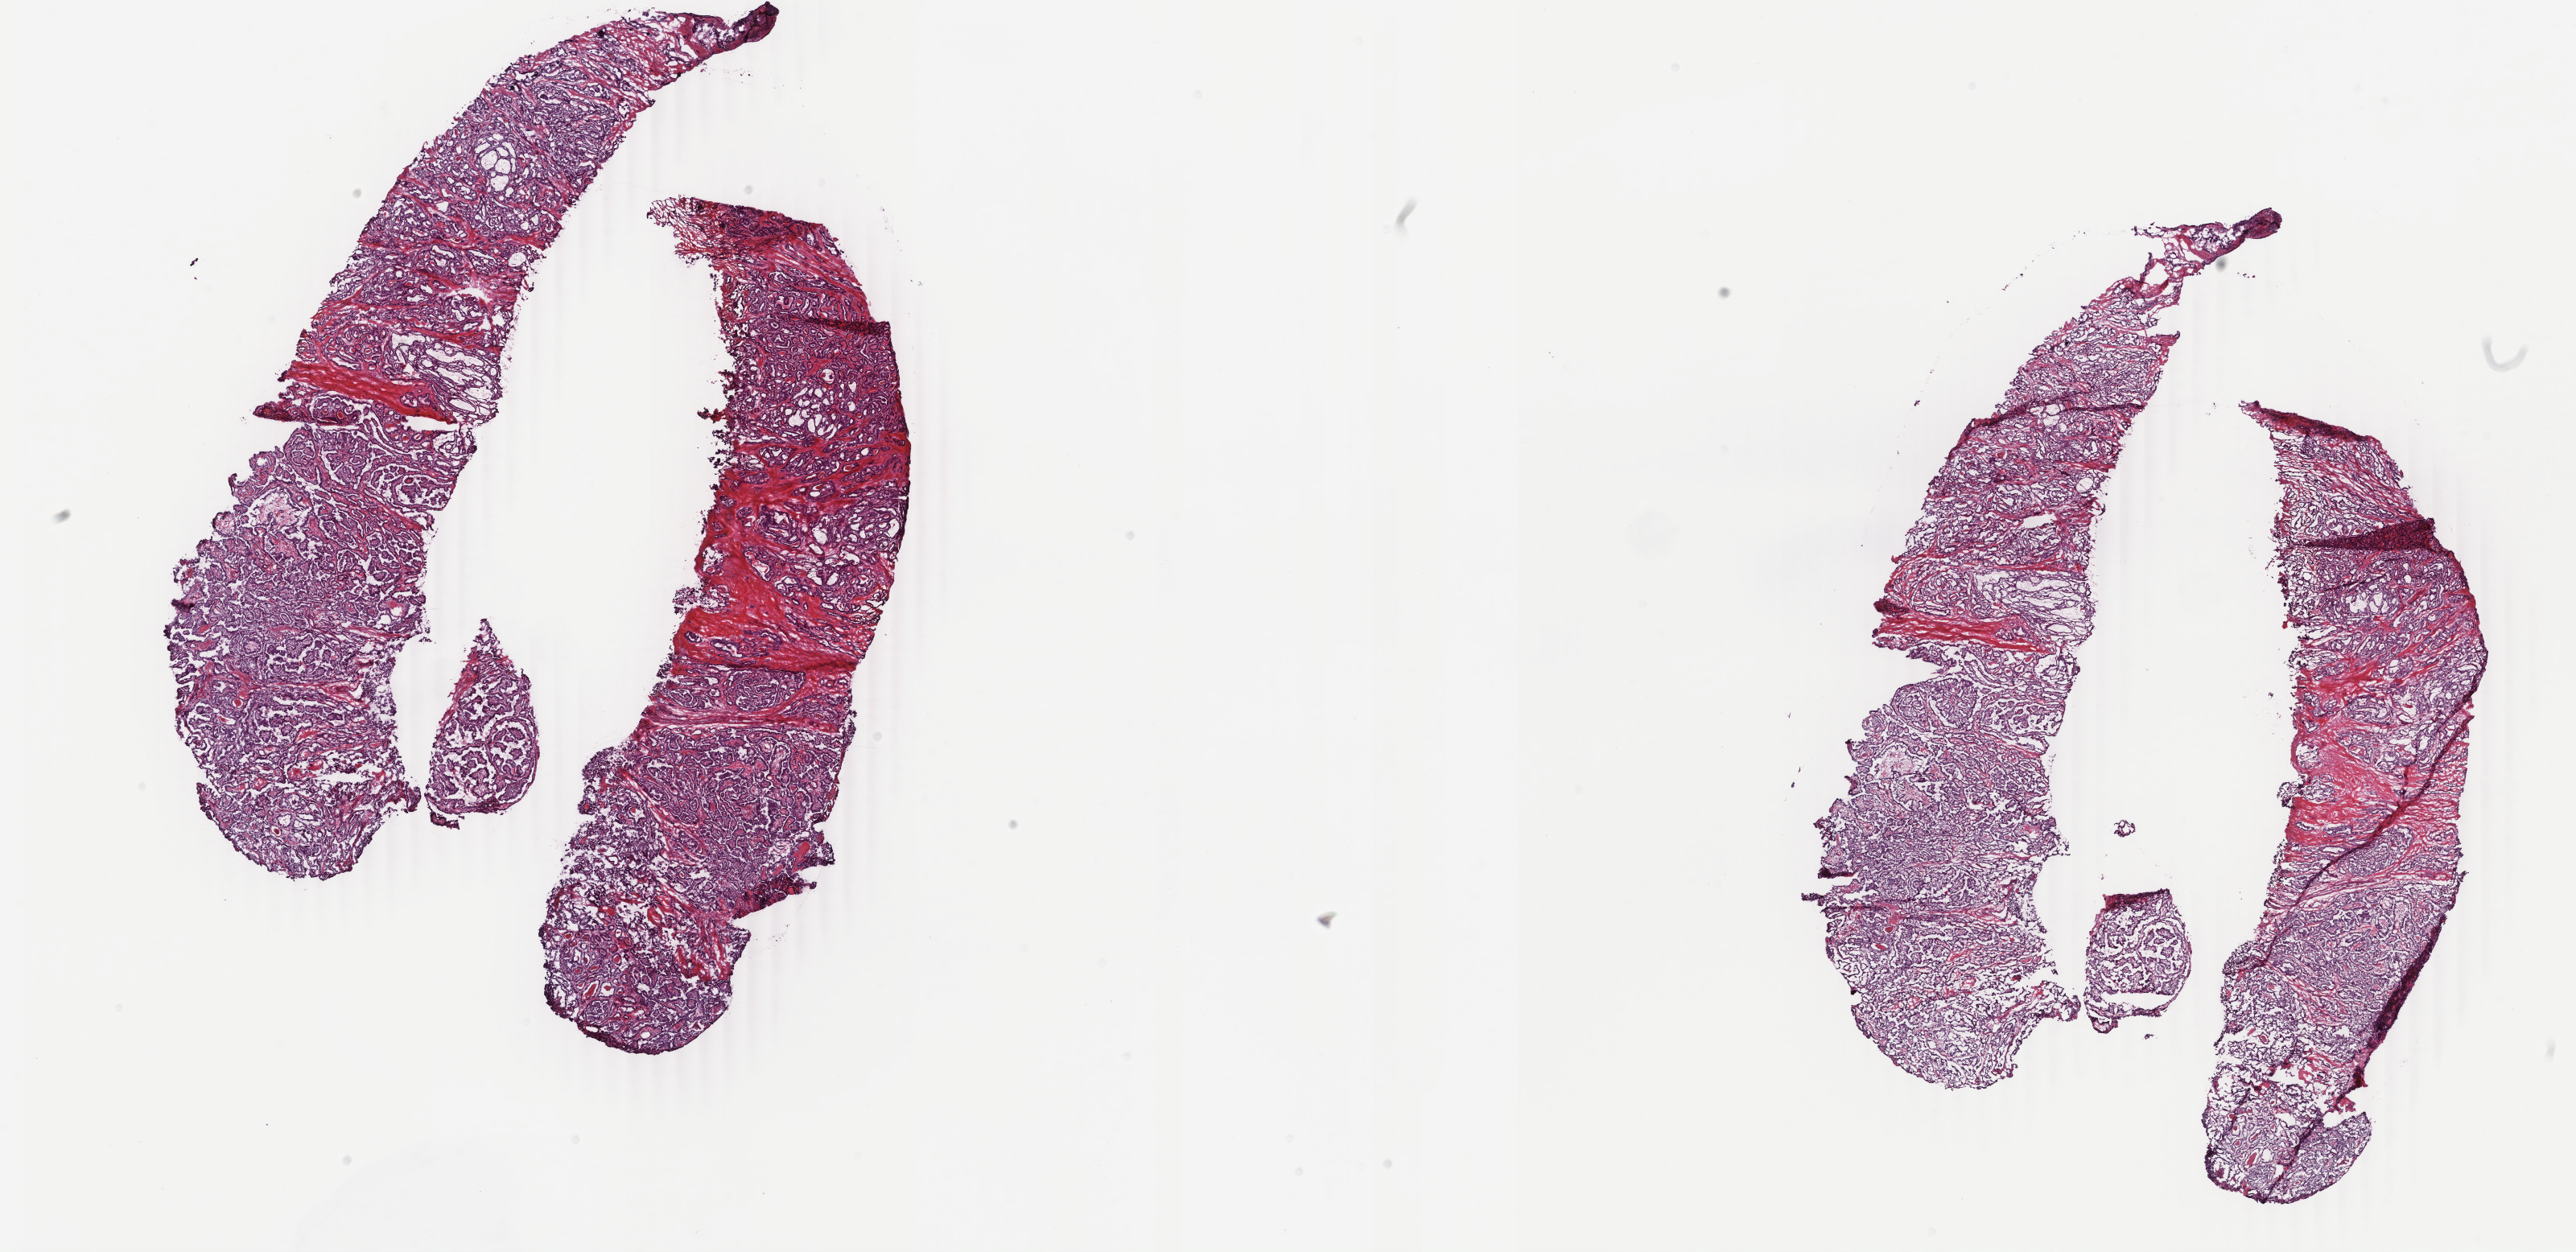
Whole-slide histology image, H&E-stained, shown as a low-resolution overview of the whole scanned area (about 25.5 x 12.4 mm, acquisition: 40x scan); frozen section from the top of the tissue portion; thyroid, primary tumour sample. Female, age 52 years at initial diagnosis. Slide review estimates, as recorded: tumour cells 100%, tumour nuclei 75%, normal cells 0%, stromal cells 0%, necrosis 0%. Inflammatory infiltration, as recorded: lymphocyte infiltration 0%, monocyte infiltration 0%, neutrophil infiltration 0%.
AJCC pathologic stage: III (7th edition). Lymph nodes positive (case pathology): 0 of 1 examined. Pathologic diagnosis: Papillary adenocarcinoma, NOS (thyroid gland).